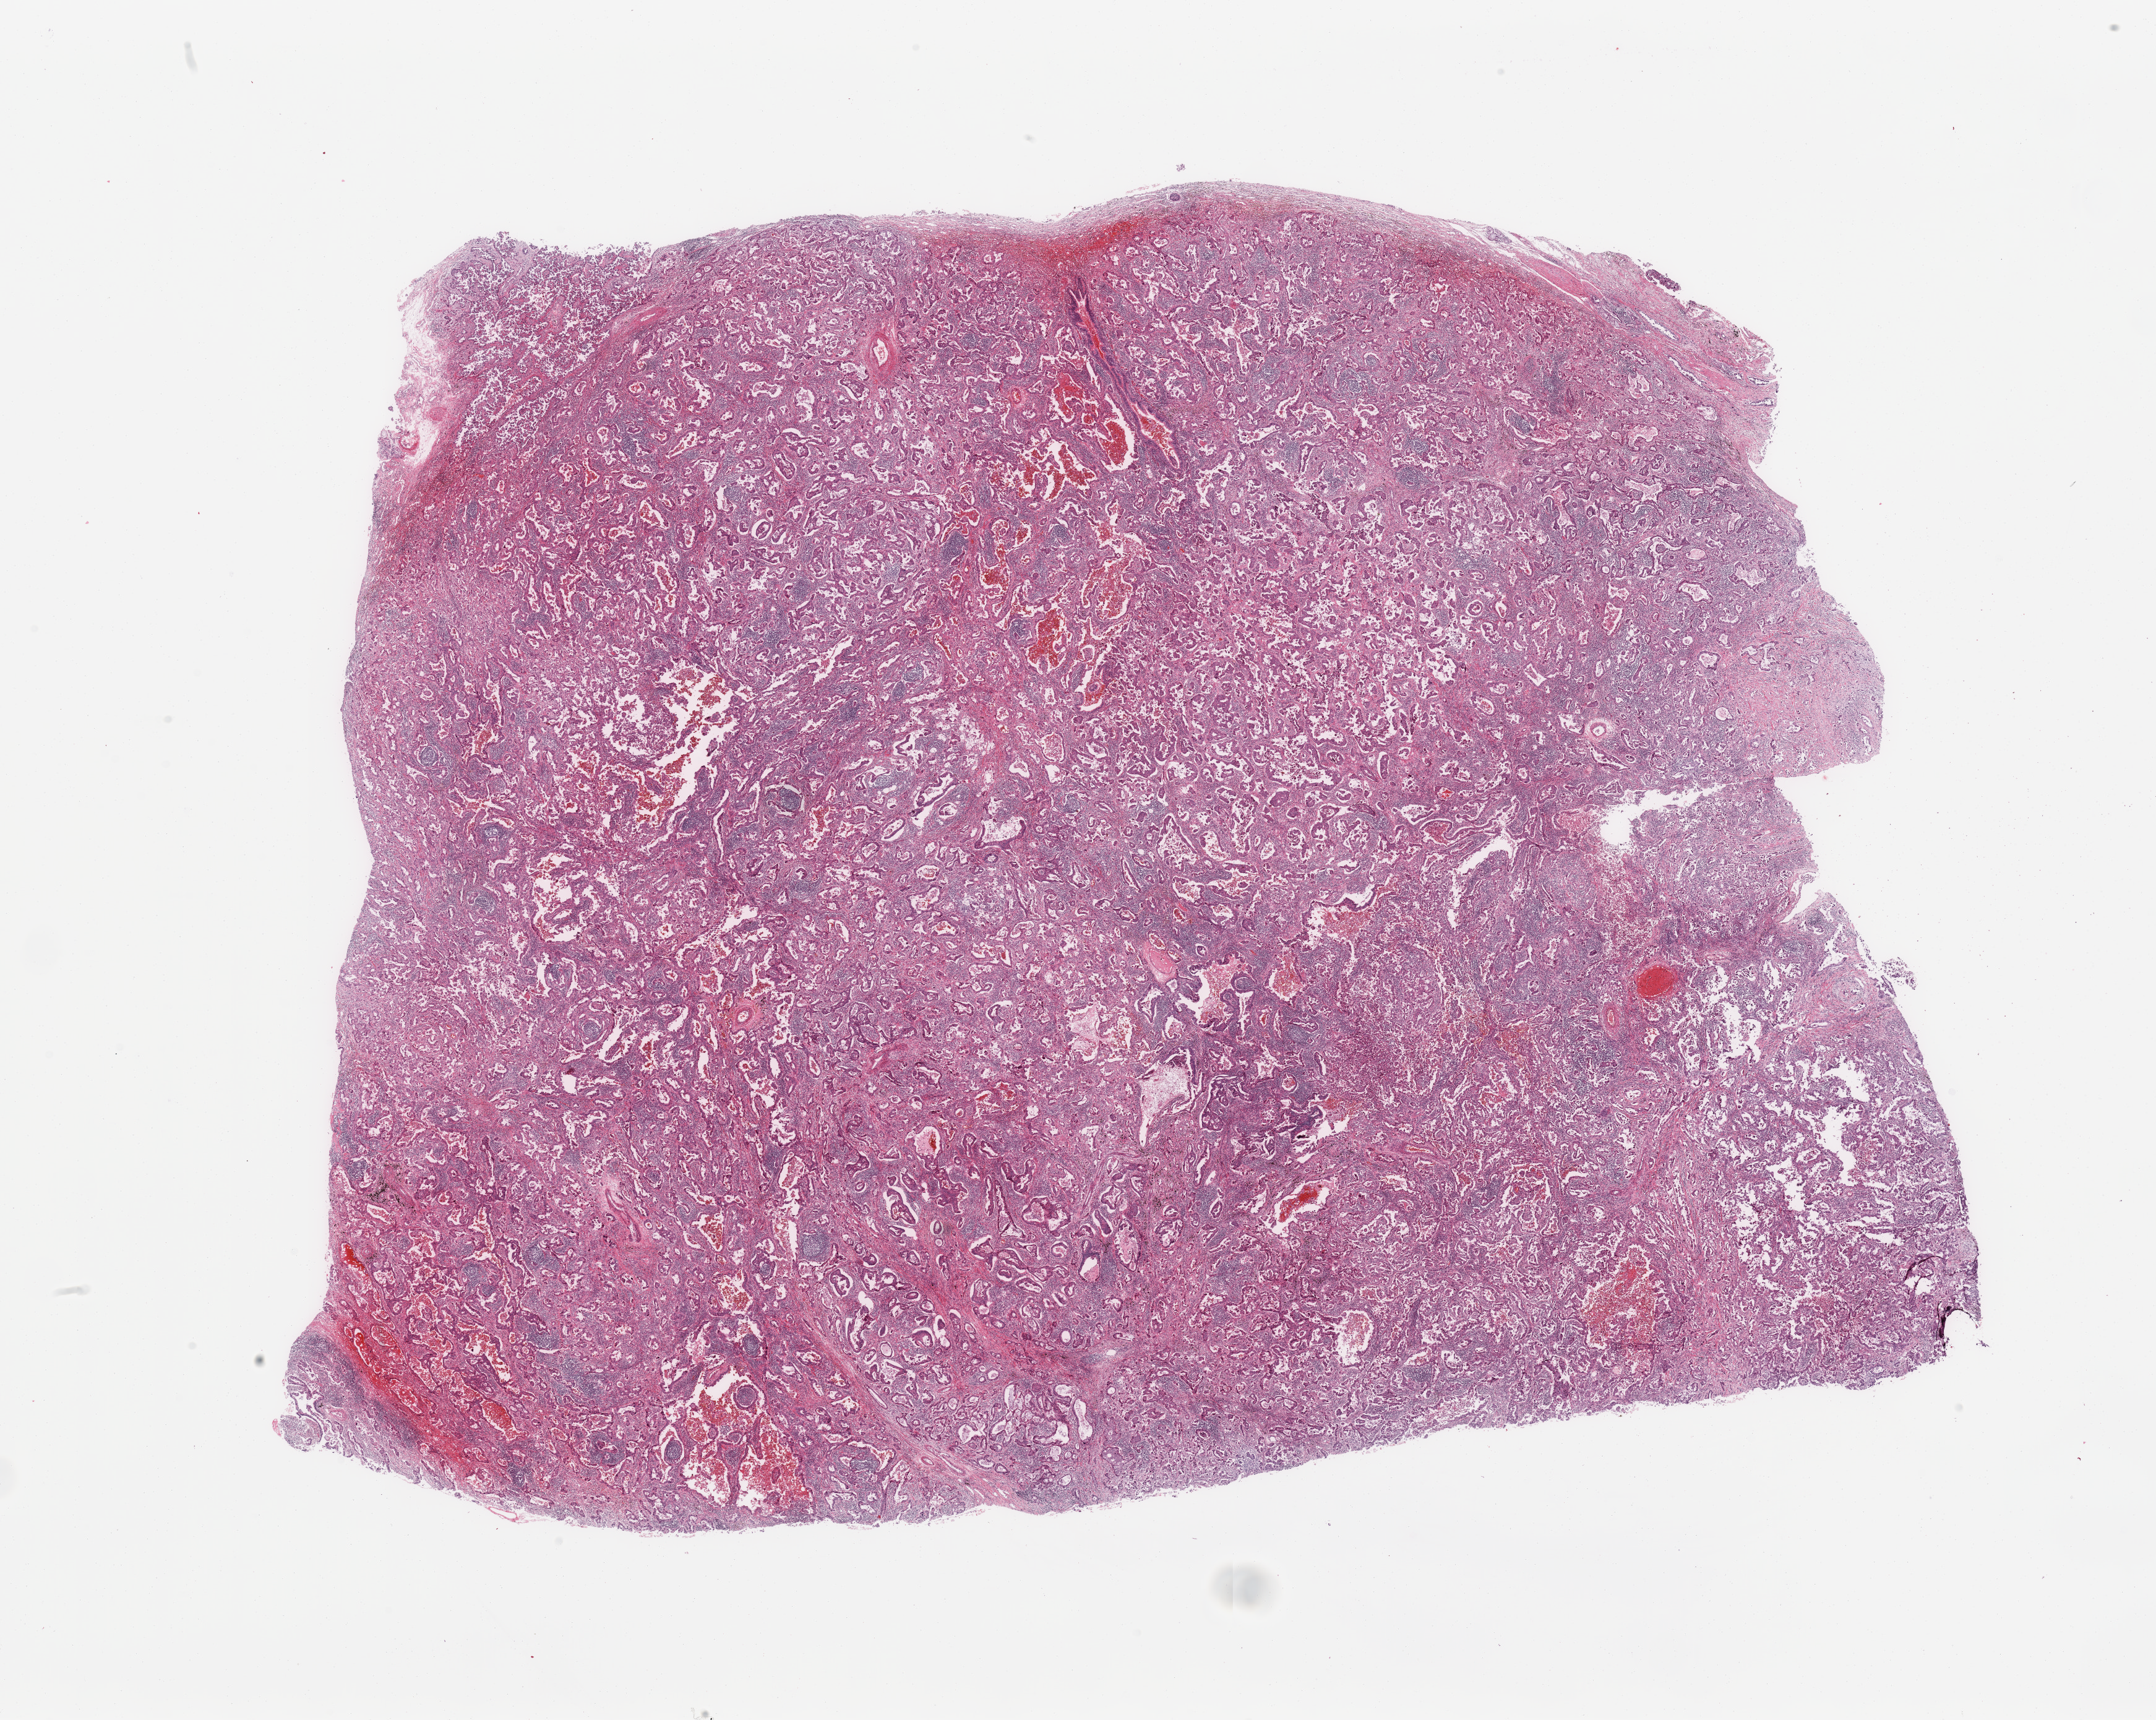
H&E-stained whole-slide image, shown as a low-resolution overview of the whole scanned area (about 27.6 x 22.0 mm, acquisition: 20x scan); tumour tissue sample, lung. Female, 72 y/o. Histologic grade: G2 (moderately differentiated).
Diagnosis: Adenocarcinoma, NOS. AJCC pathologic stage: IIIA.